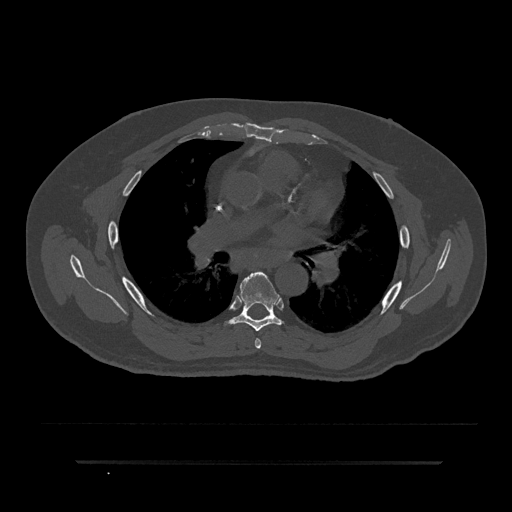
CT including the spine, one axial slice. Slice 532 of 797 in the series (ordered by position). Reconstruction kernel Br40s/3. Bone window (W 1800 / L 400 HU). 0.5 mm slice thickness. 512 × 512 image matrix. Patient: male, 59 years. From the clinical record (not read from this slice): primary cancer: bile ducts; vertebrae with lytic lesions (as recorded): T10.
Structures marked on this image (semi-automatically segmented with operator editing):
- T5 vertebra: bounding box (x1, y1, x2, y2) in pixels: (255, 338, 262, 349)
- T6 vertebra: (227, 272, 283, 332)